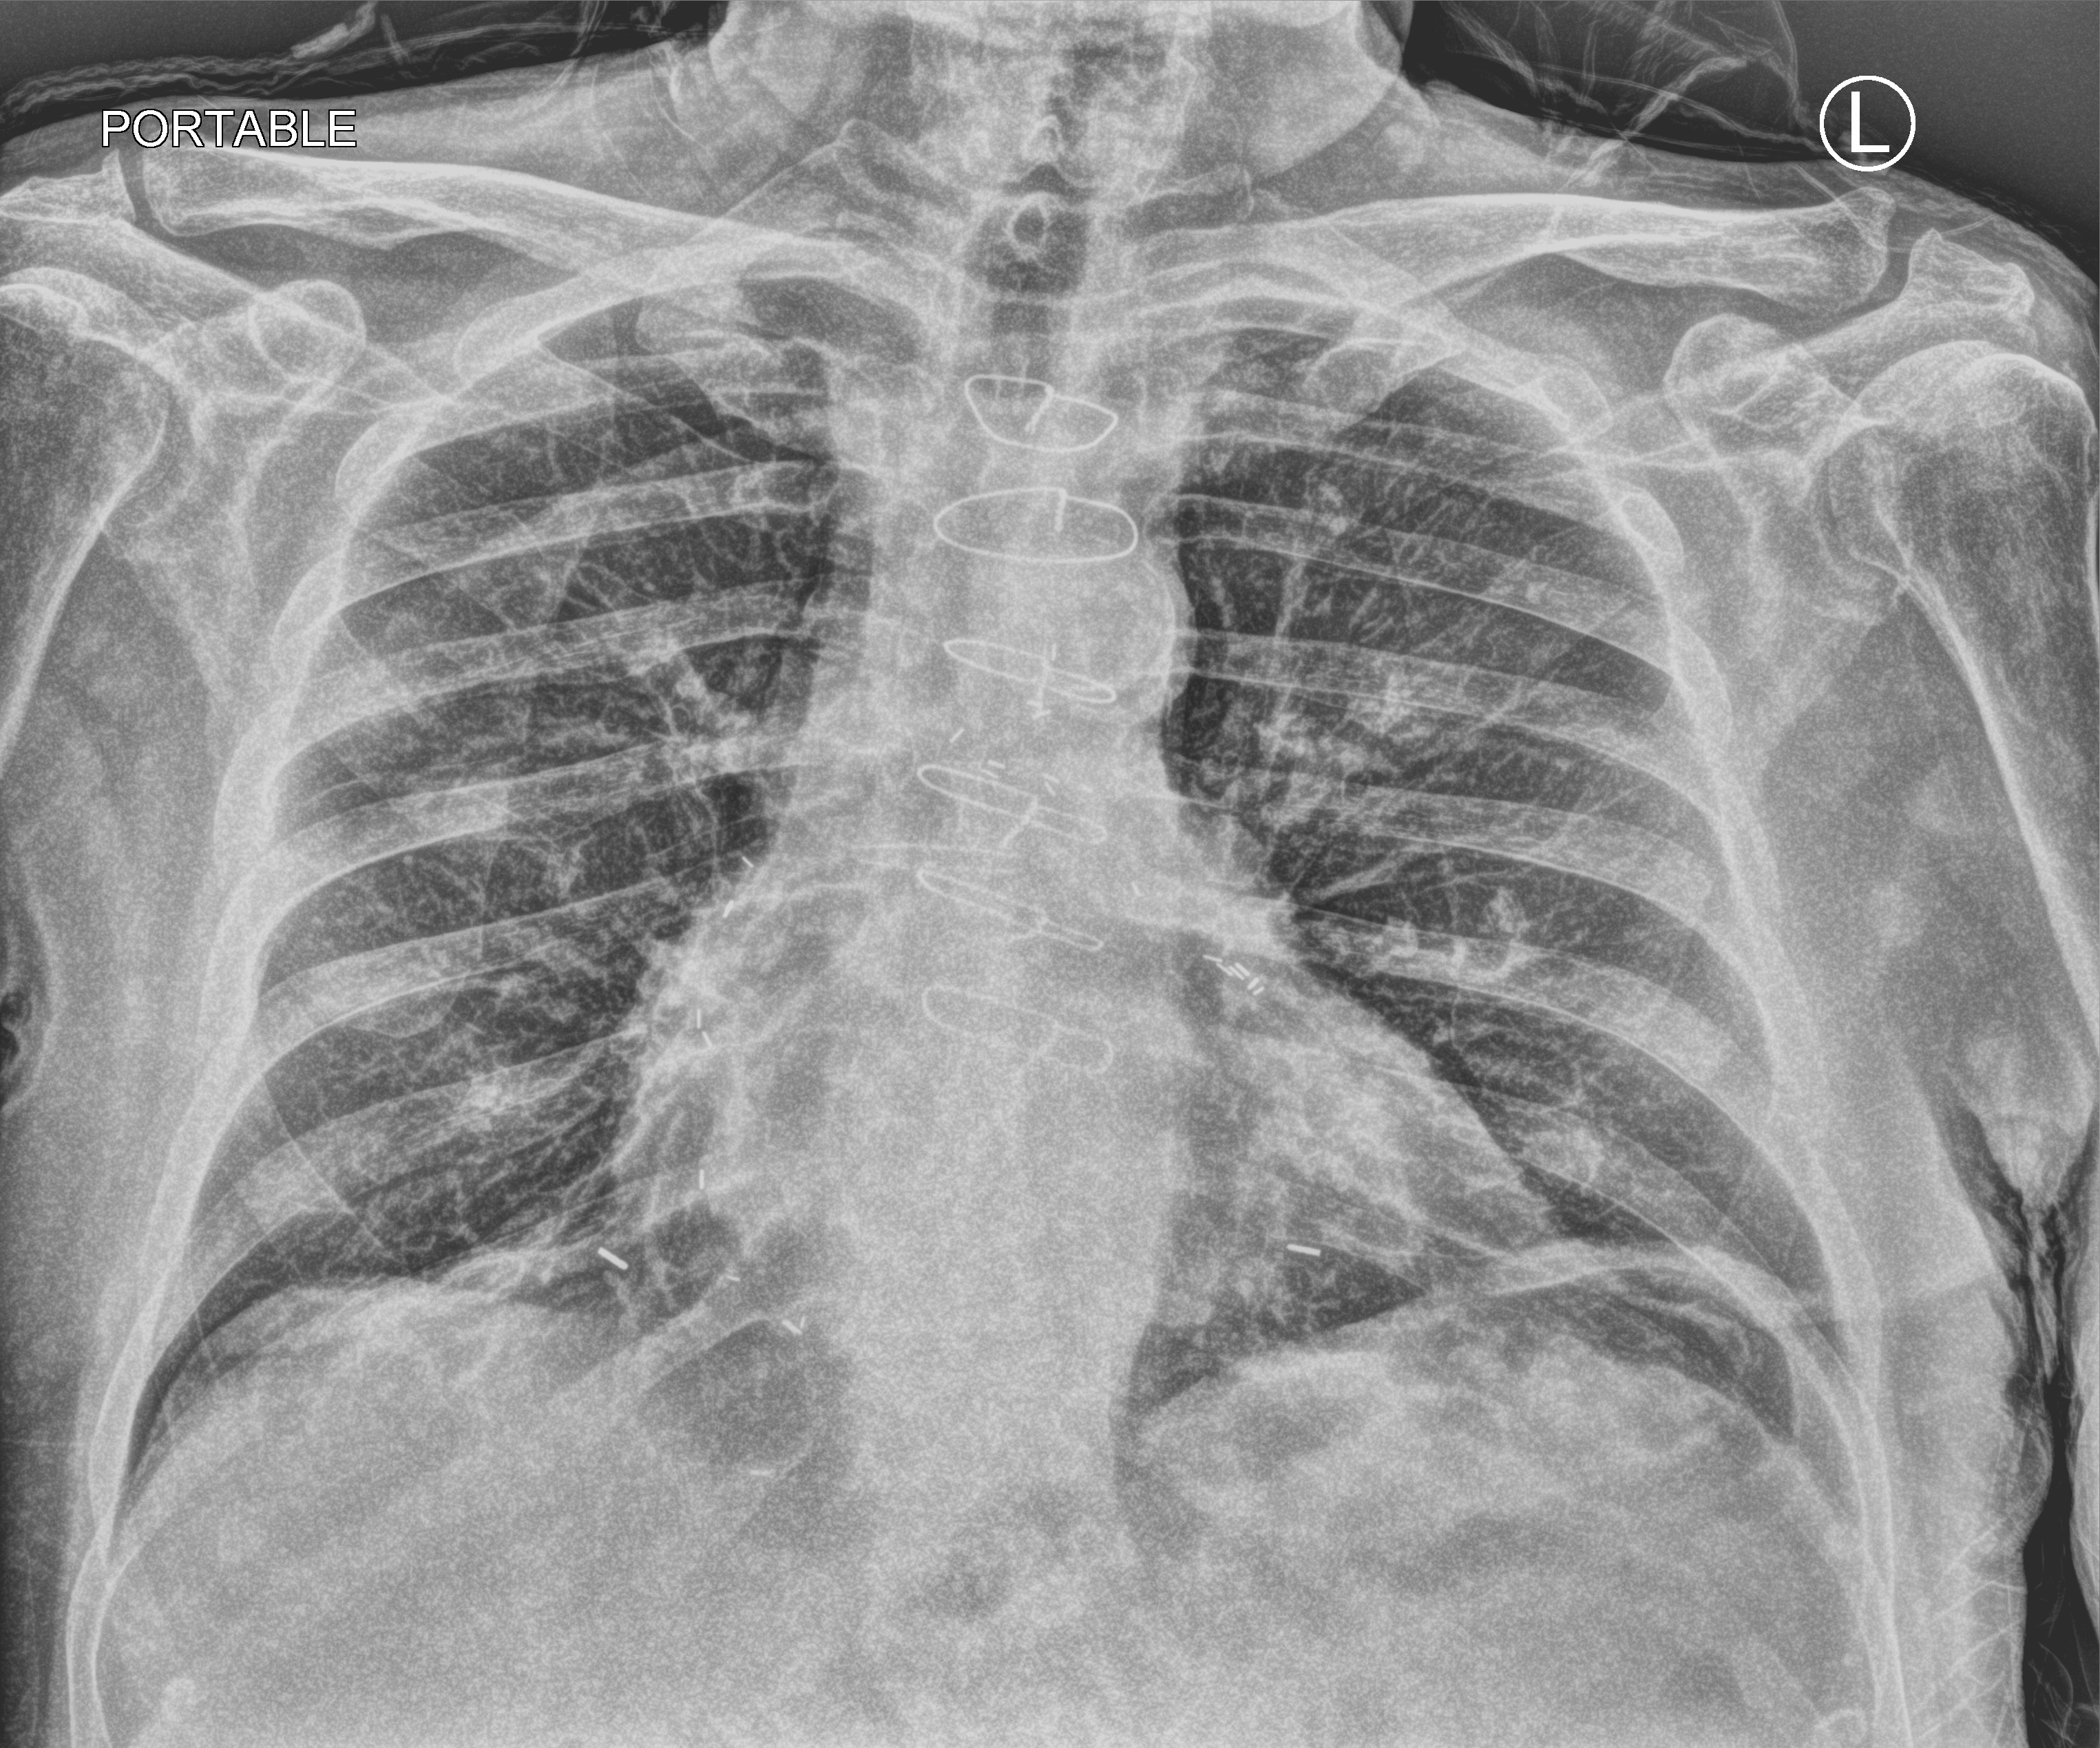
Chest X-ray (portable); anteroposterior (AP) projection. Male patient hospitalised with COVID-19, age 75–90 years.
From the hospital-stay record, not from the radiograph (when in the stay this image was taken is not recorded): mechanically ventilated during this hospital stay: yes; admitted to intensive care during this hospital stay: yes; hypertension (admission record): yes.